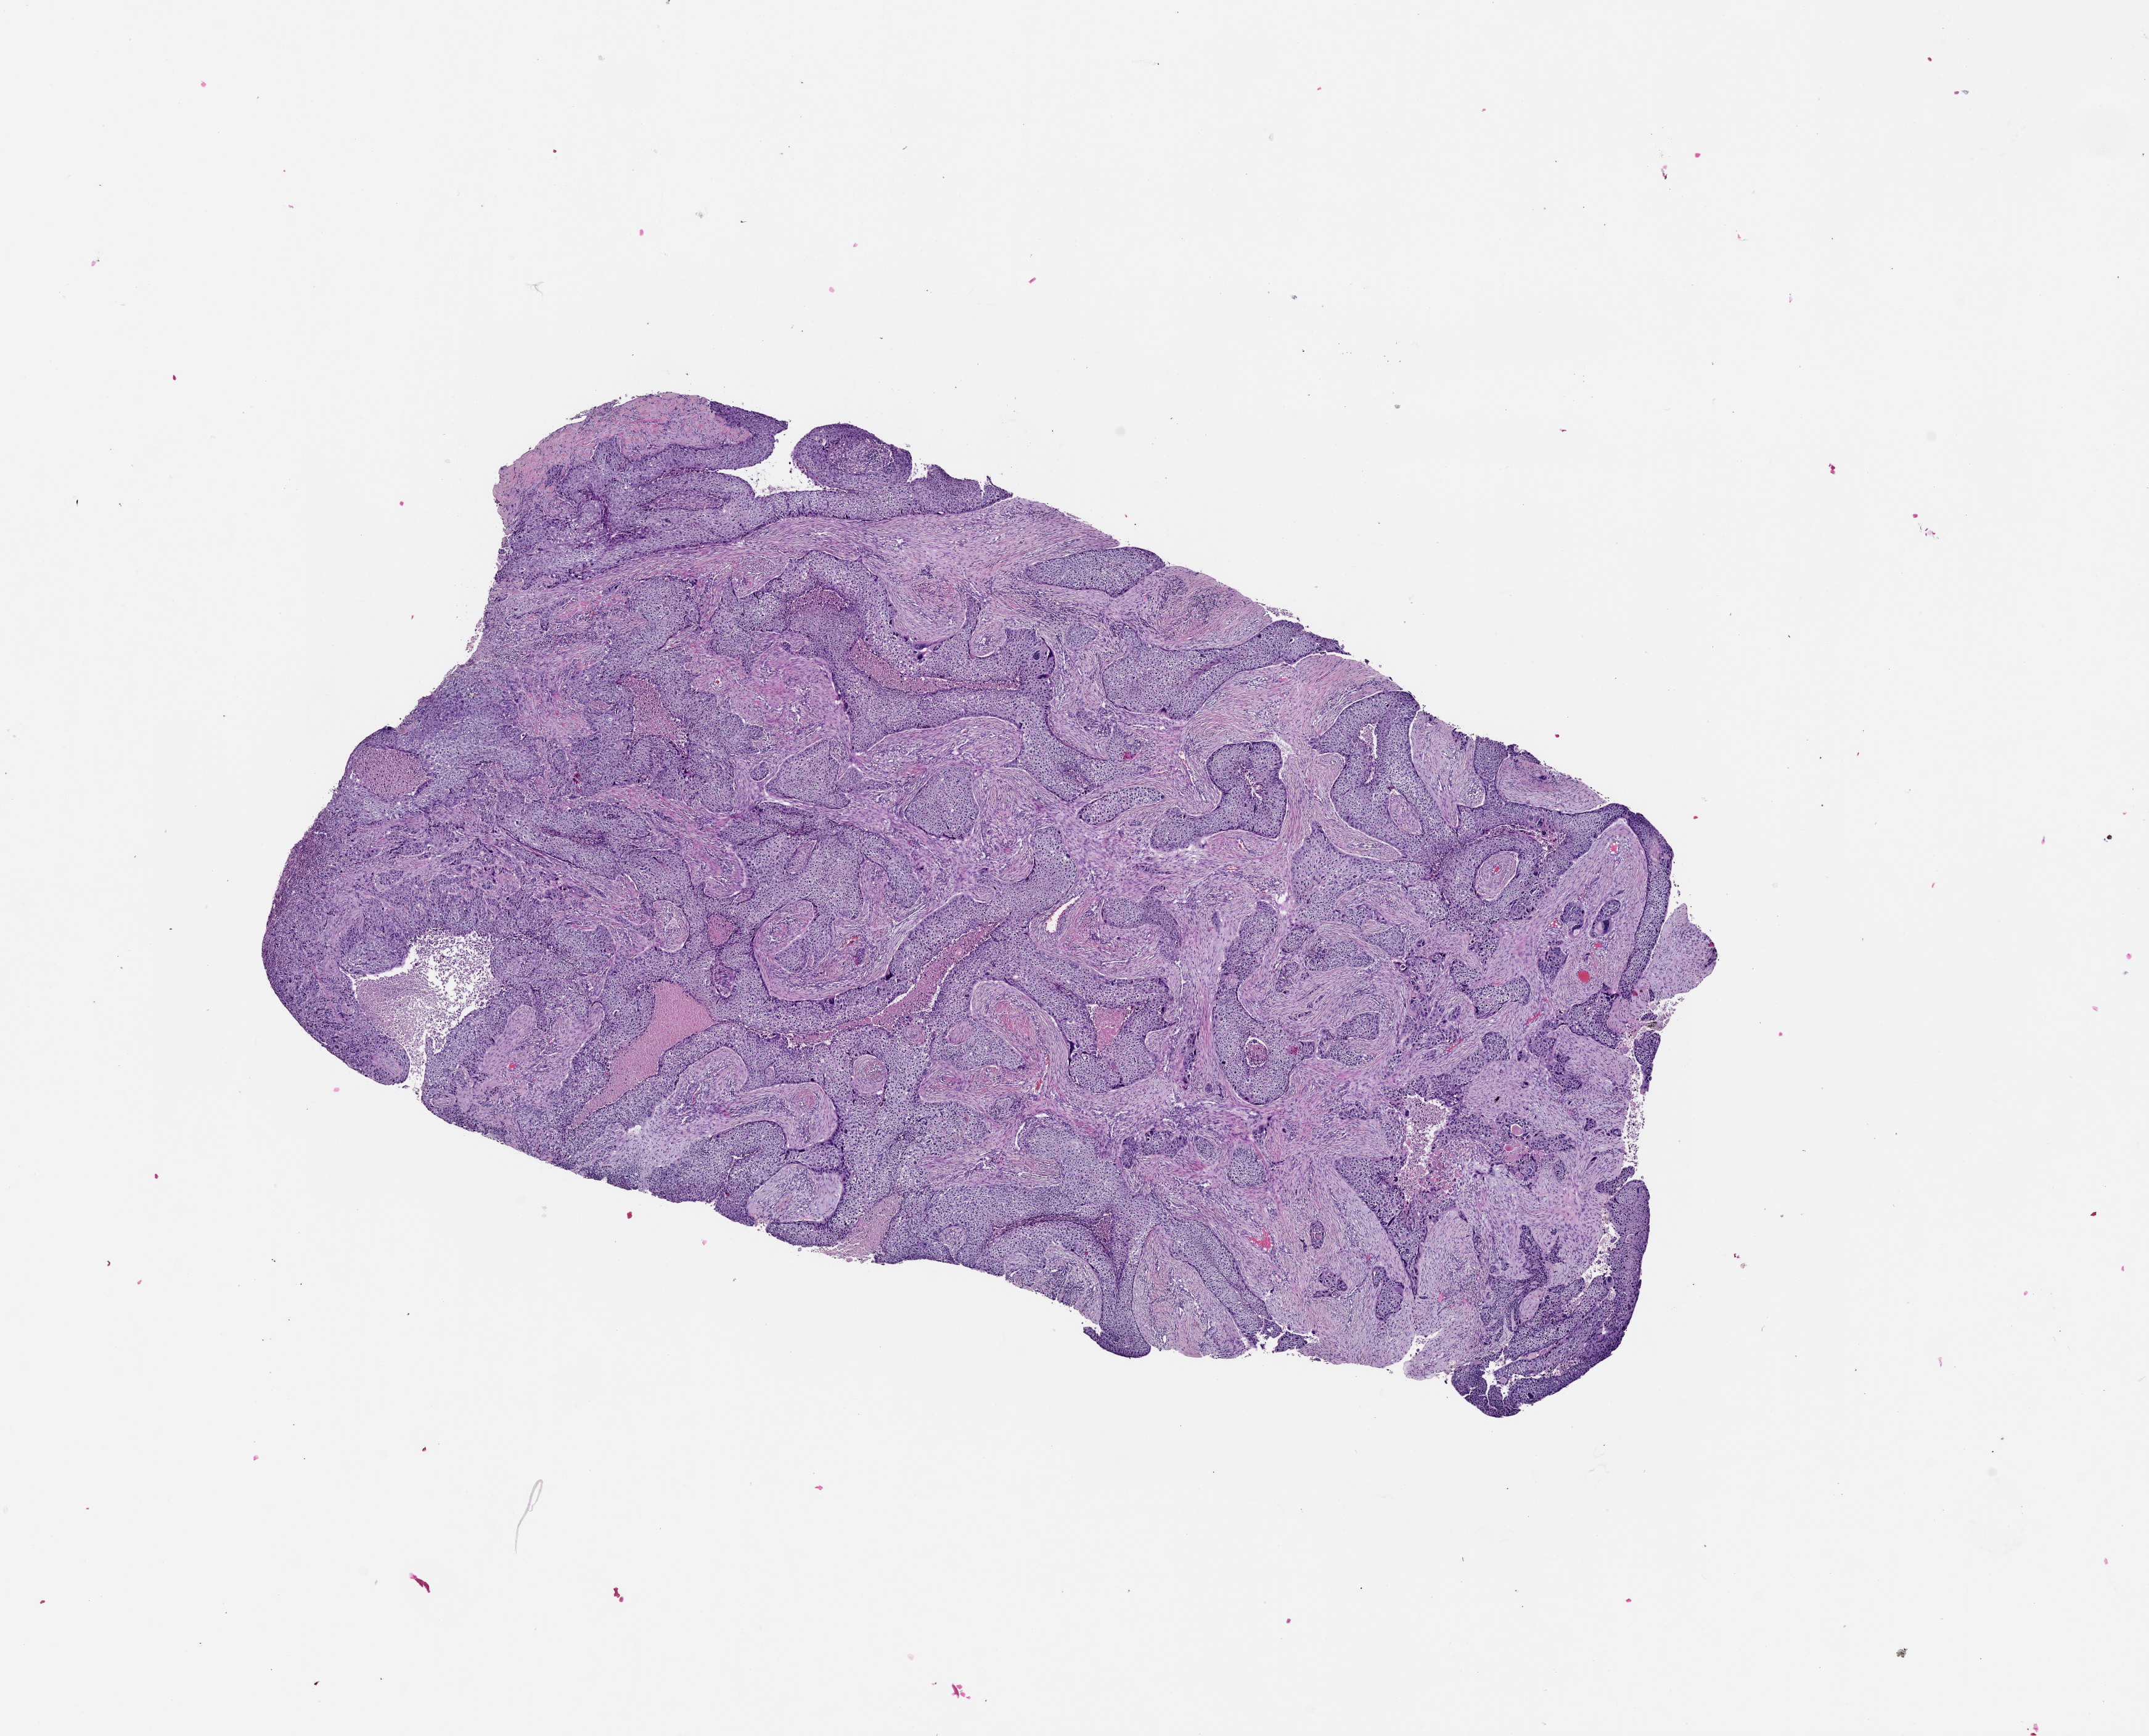
Whole-slide histology image, H&E — shown as a low-resolution overview of the whole scanned area (about 14.0 x 11.3 mm, slide scanned at 20x). Tumour tissue sample, lung. Male, 55 y/o.
• patient diagnosis (cohort enrolment): squamous cell carcinoma (lung)